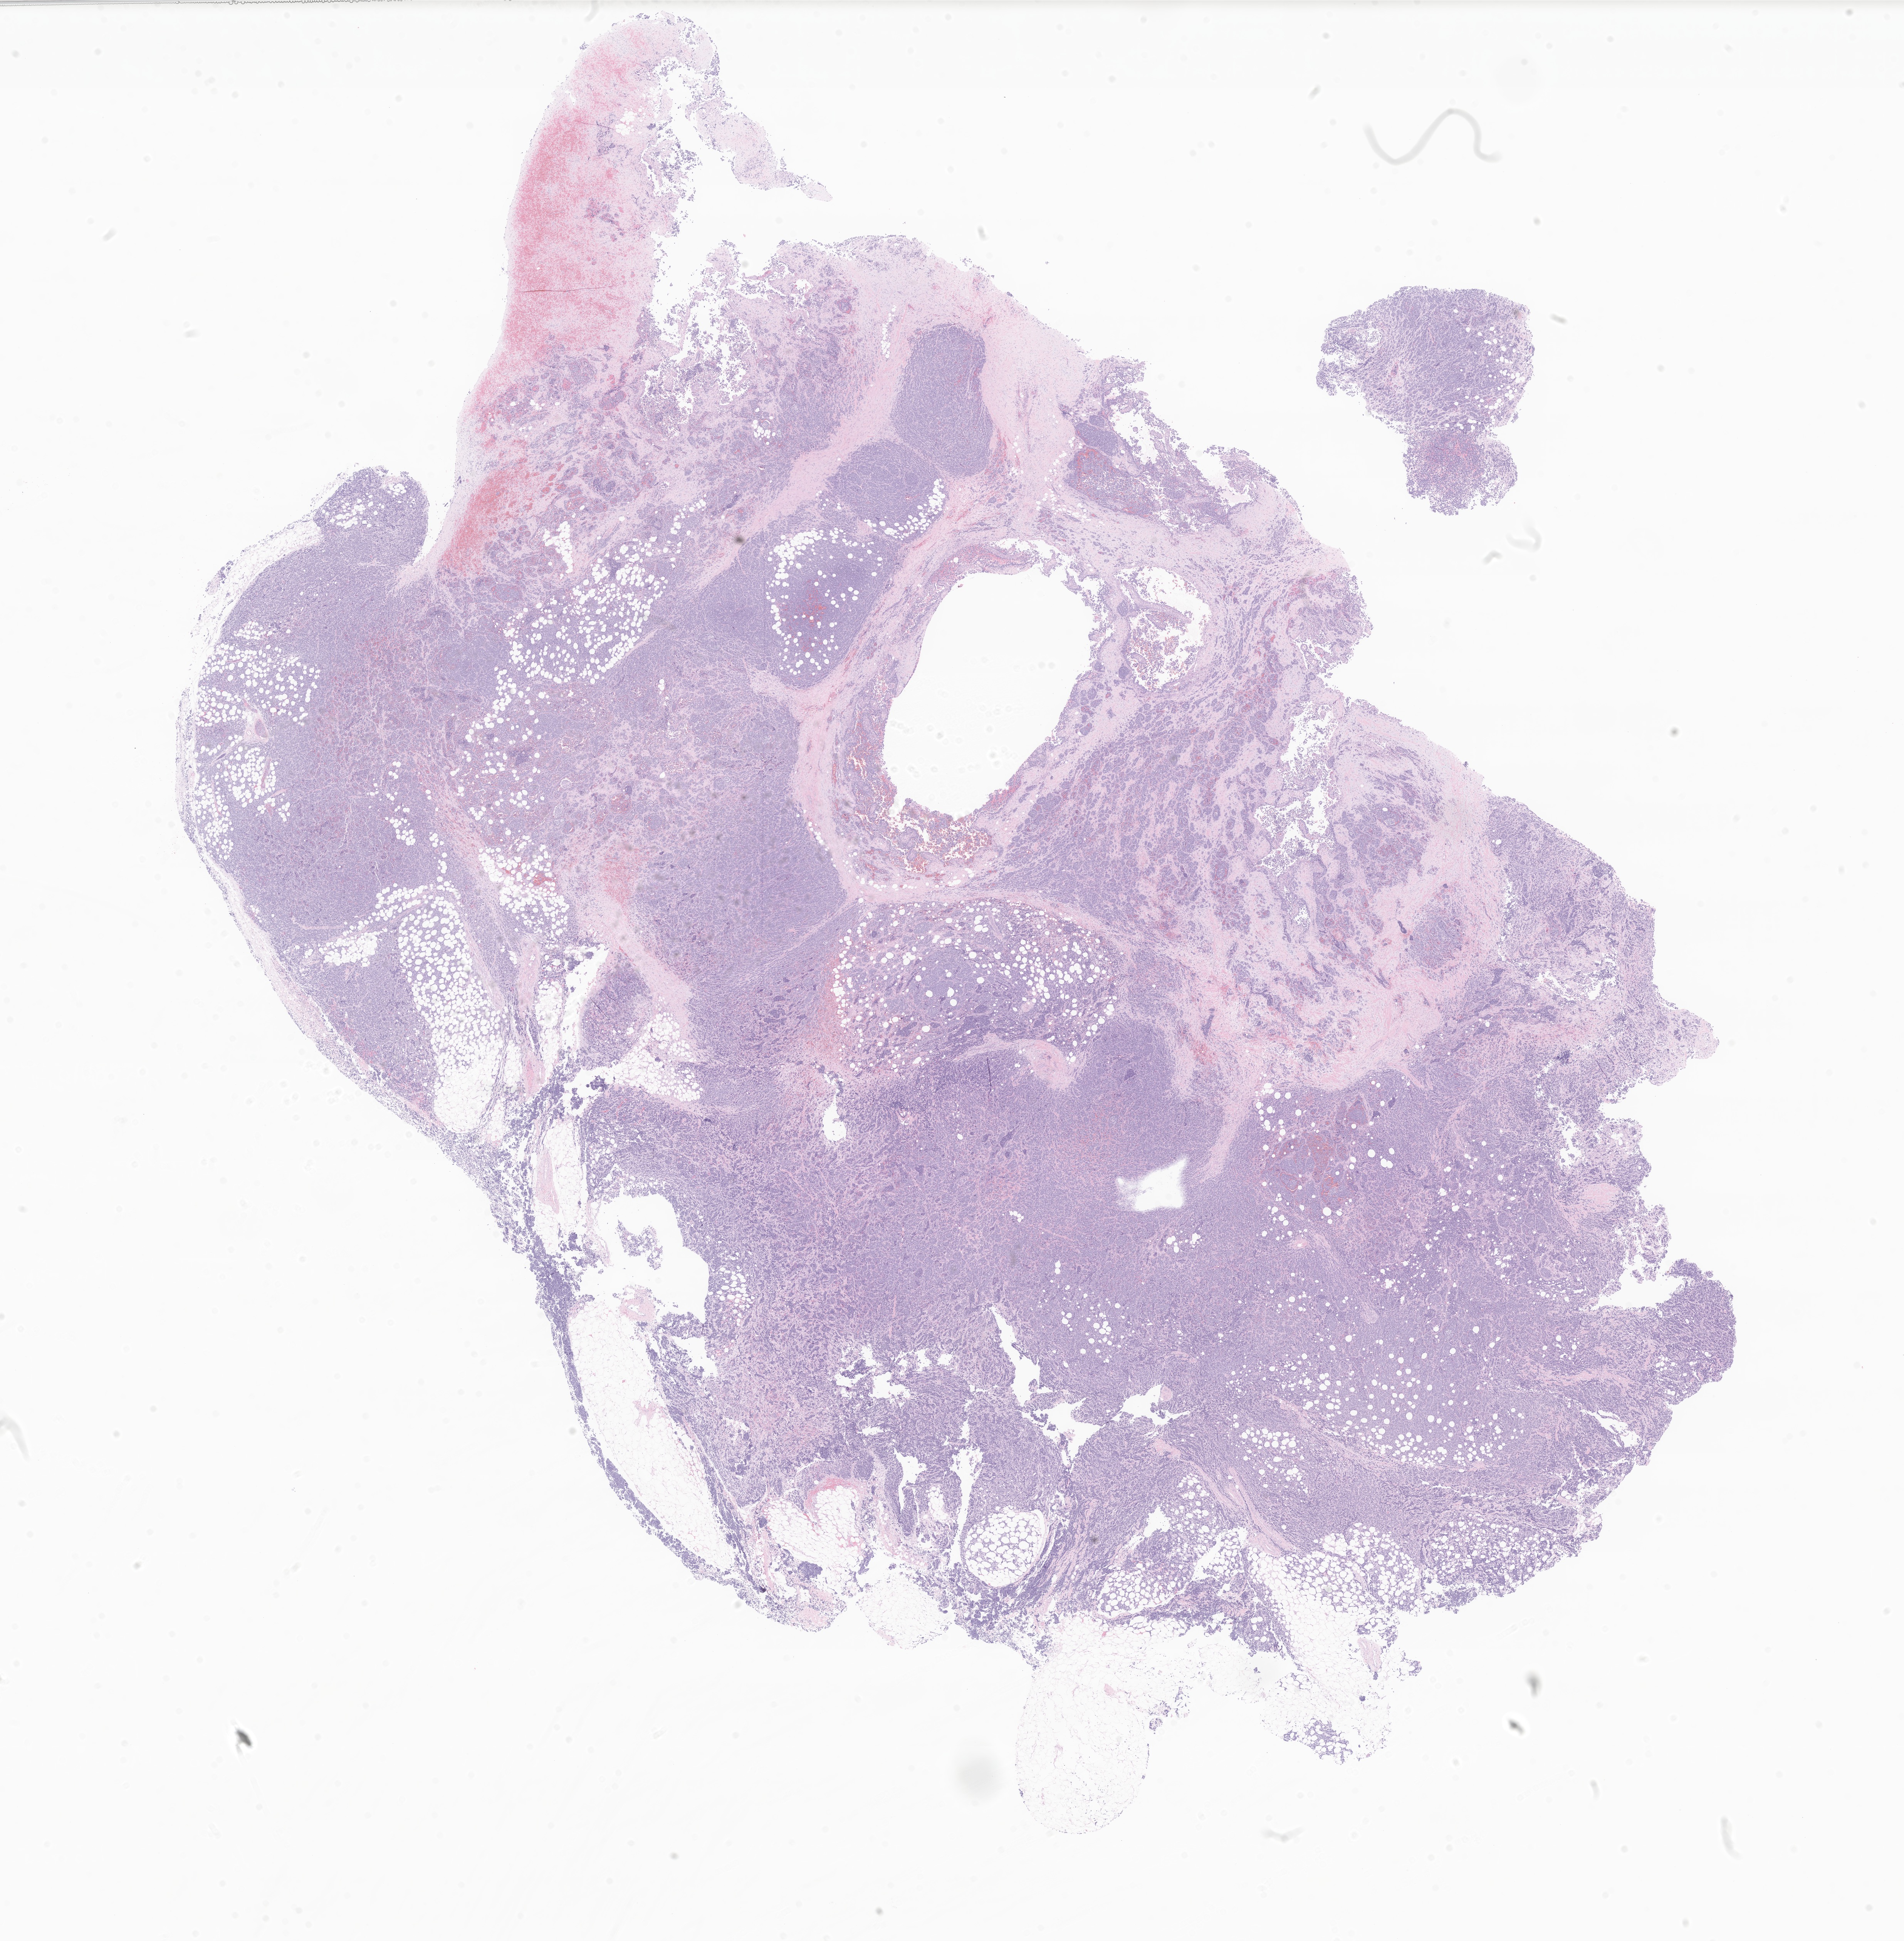
Whole-slide image, hematoxylin and eosin (H&E) stain of tumor tissue from the lower limb lymph node — a low-resolution overview of the entire scanned area, about 20.8 x 21.2 mm; formalin-fixed paraffin-embedded section. Patient male; age 982 days.
* tissue or organ of origin (case record): lymph nodes of inguinal region or leg
* diagnosis (ICD-O-3 morphology term): Alveolar rhabdomyosarcoma